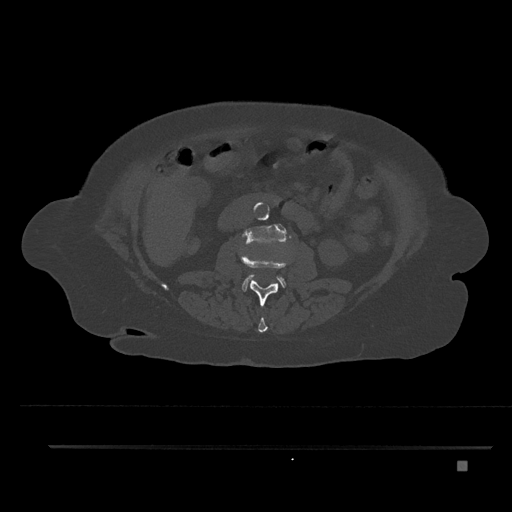
CT including the spine, one axial slice; slice 165 of 797 in the series (ordered by position); reconstruction kernel Br40s/3; bone window (W 1800 / L 400 HU); 512 × 512 image matrix, field of view 437 × 437 mm. Patient: female, 76 years. From the clinical record (not read from this slice): primary cancer: lung; vertebrae with lytic lesions (as recorded): T11, L3.
Structures marked on this image (semi-automatic segmentation, software-assisted and operator-edited):
- L1 vertebra: bounding box (x1, y1, x2, y2) in pixels: (248, 299, 267, 333)
- L2 vertebra: (241, 252, 292, 307)
- L3 vertebra: (242, 224, 286, 292)